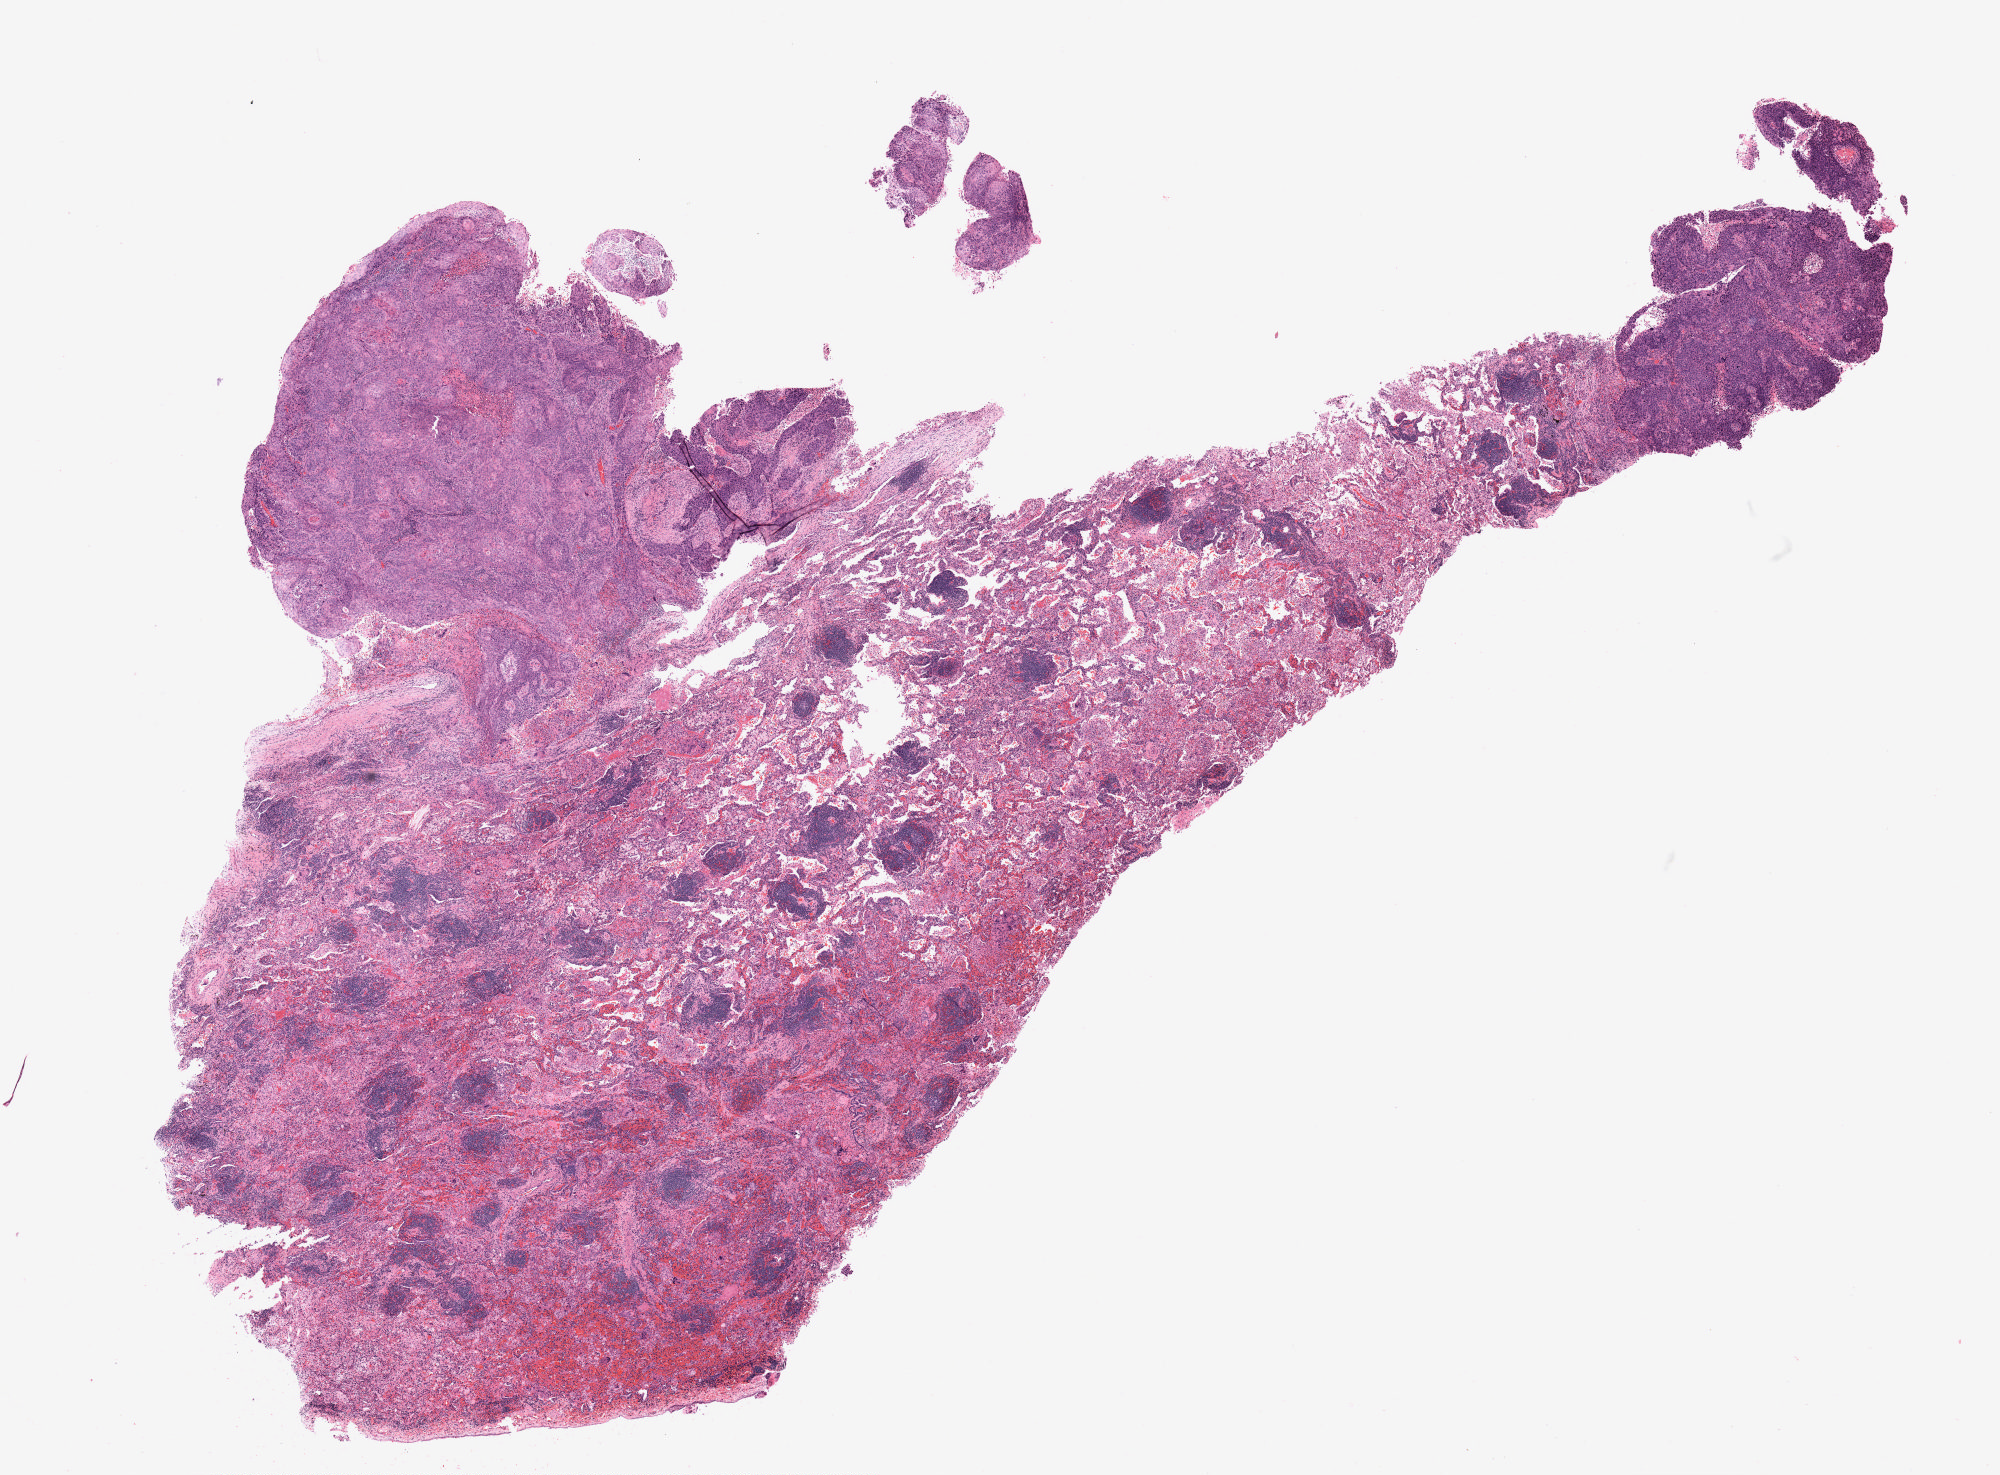
Digitized H&E-stained tissue section (whole slide), shown as a low-resolution overview of the whole scanned area (about 16.0 x 11.8 mm); formalin-fixed paraffin-embedded (FFPE) diagnostic section; primary tumour sample from the lung. Male, age 54 years at initial diagnosis.
AJCC pathologic stage: IB (7th edition). Laterality: right. Diagnosis: Squamous cell carcinoma, keratinizing, NOS.